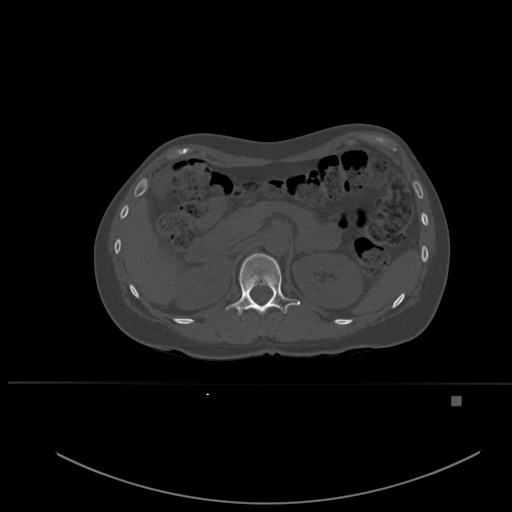
CT including the spine, one axial slice. Position 254 of 651 along the scan axis. Bone window (W 1800 / L 400 HU). 512 × 512 image matrix. Patient: female, 49 years. Case-level facts recorded for this patient, not image findings: primary cancer: breast; vertebrae with lytic lesions (as recorded): L3, T12, L4.
Outlined on this slice (semi-automatically segmented with operator editing):
- T12 vertebra: bounding box (x1, y1, x2, y2) in pixels: (225, 253, 300, 316)